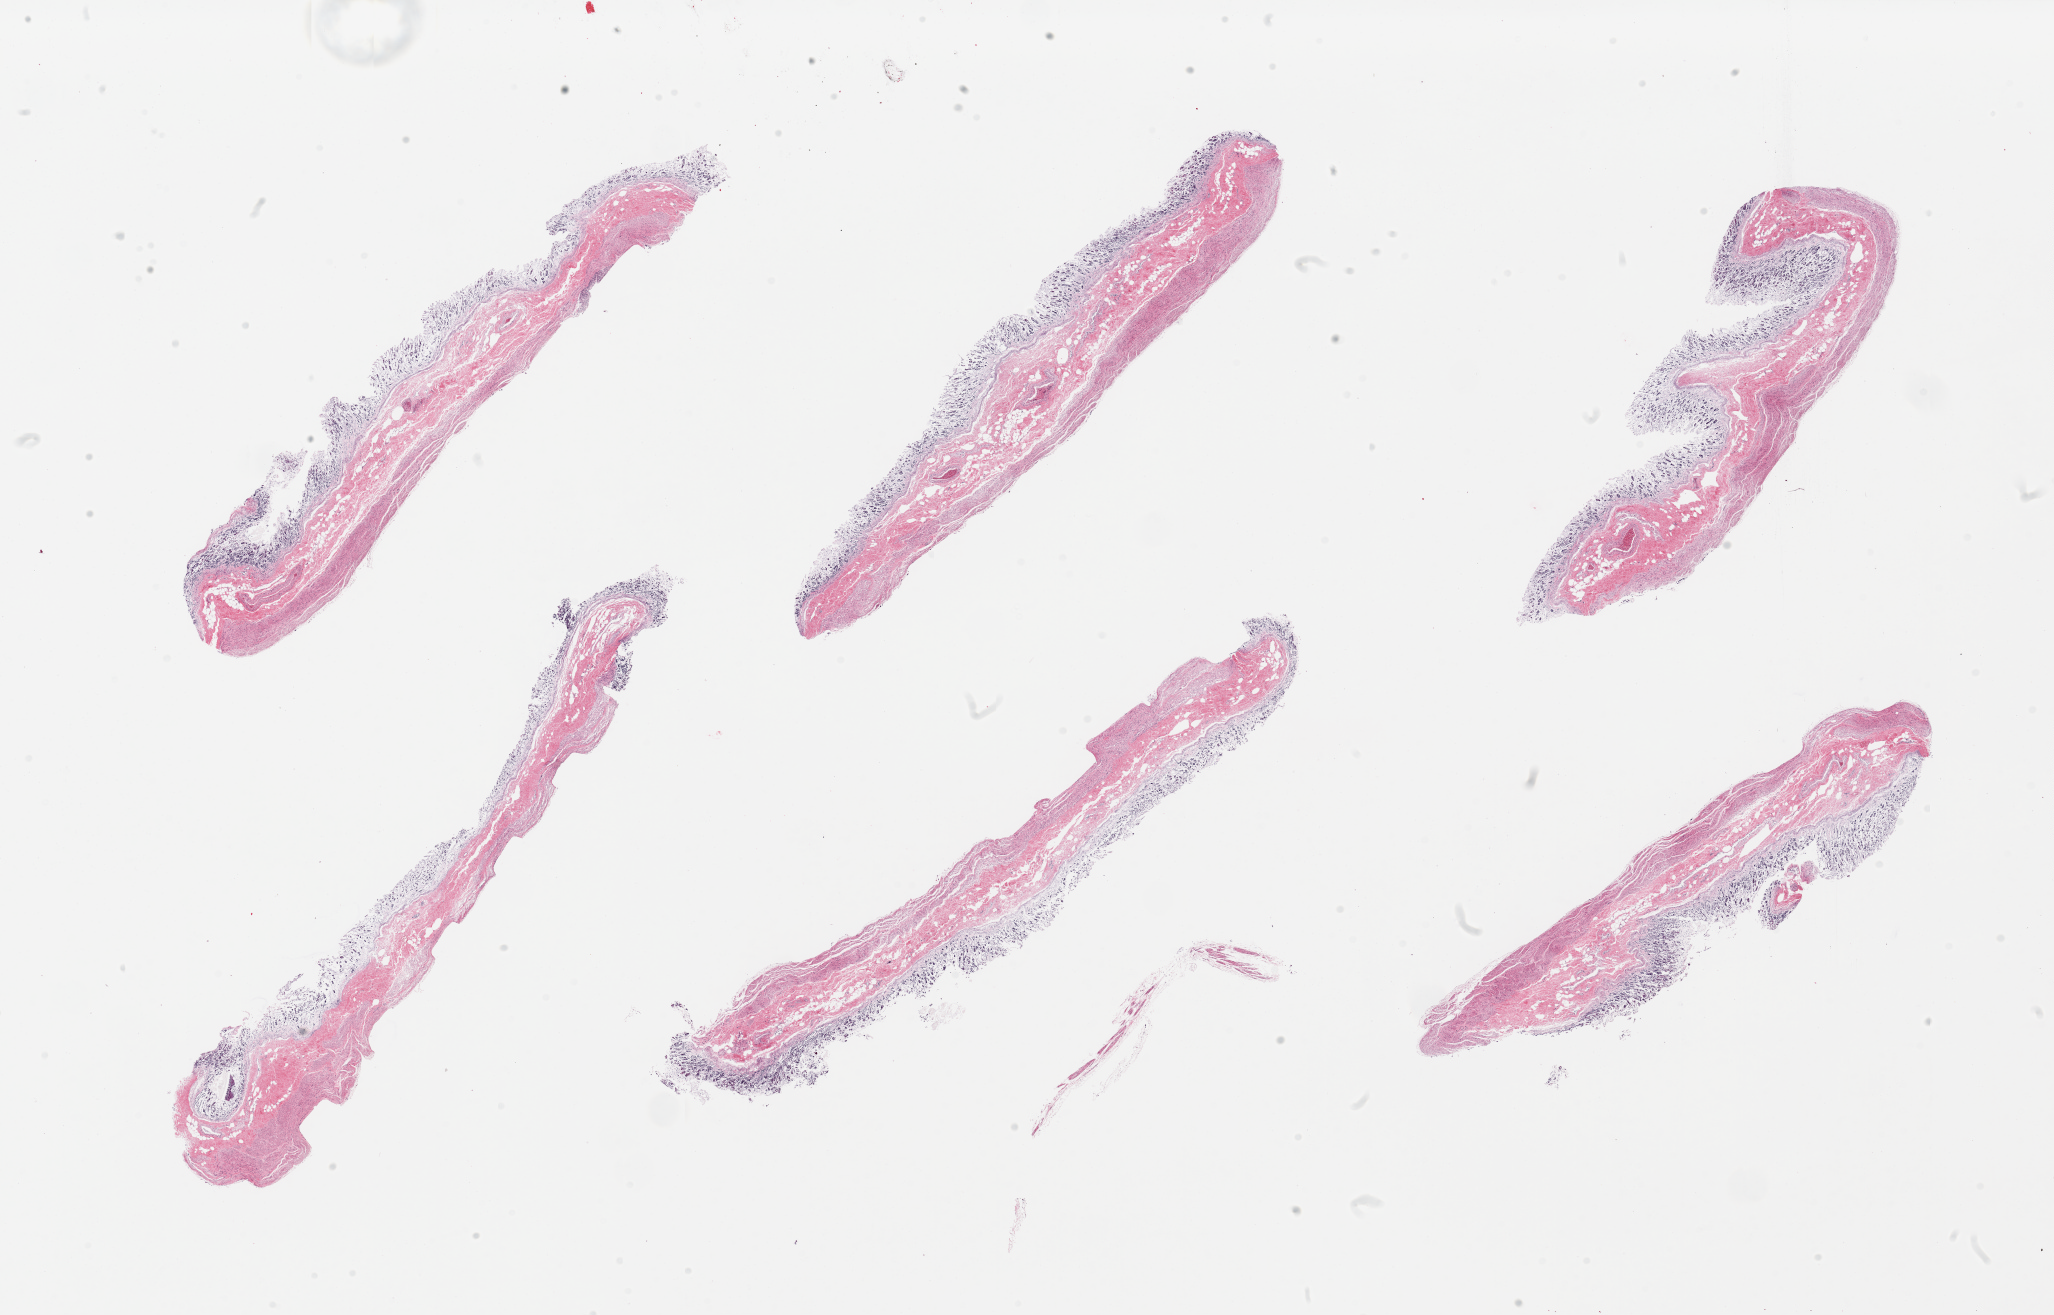
Digitized H&E-stained section, whole scanned area (about 32.5 x 20.8 mm) shown as a low-resolution overview; PAXgene-fixed paraffin-embedded (PFPE) section; section of stomach (target tissue); donor tissue sample. Male donor.
* review note (as recorded): 6 pieces, mucosa up to ~0.5mm, totally autolyzed